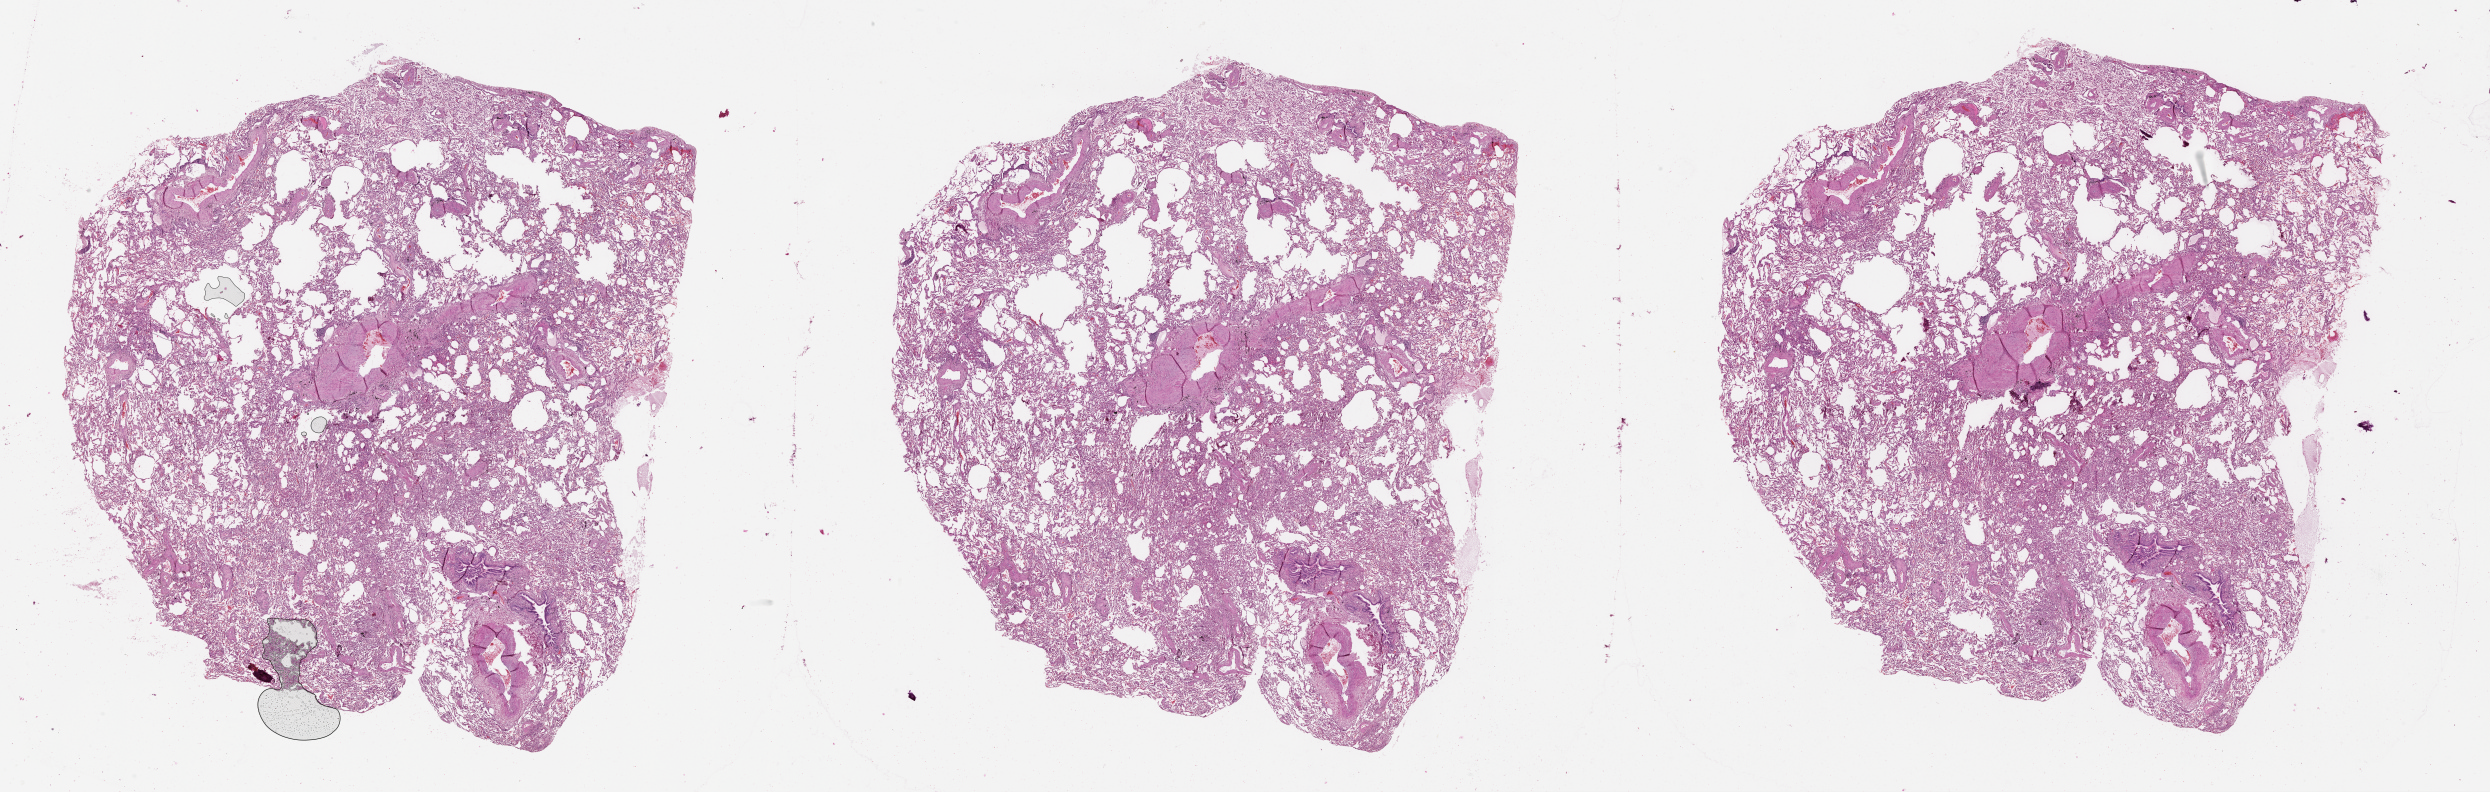
Digitized H&E tissue section (whole slide) — a low-resolution overview of the entire scanned area, about 40.1 x 12.8 mm; lung, normal (non-tumour) tissue. 71-year-old male patient.
This section: normal (non-tumour) tissue from the same patient. Patient diagnosis (cohort enrolment): squamous cell carcinoma (lung).